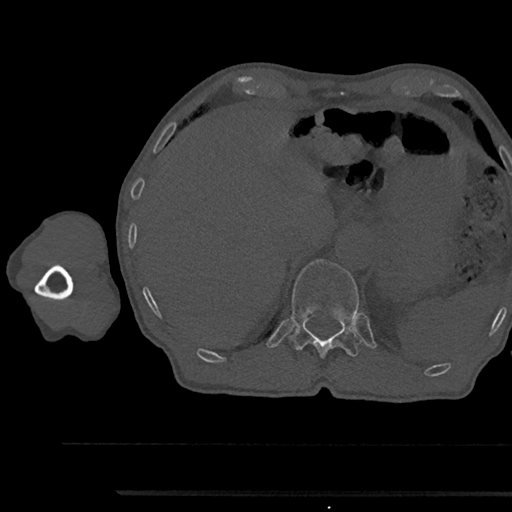
CT including the spine, one axial slice. Position 718 of 797 along the scan axis. Bone window (W 1800 / L 400 HU). 0.5 mm slice thickness. 512 × 512 image matrix. Patient: male, 79 years. Case-level facts recorded for this patient, not image findings: primary cancer: prostate.
Annotated regions visible in this slice (semi-automatically segmented with operator editing):
- T12 vertebra: bounding box <291,259,361,359> (left, top, right, bottom; pixels)